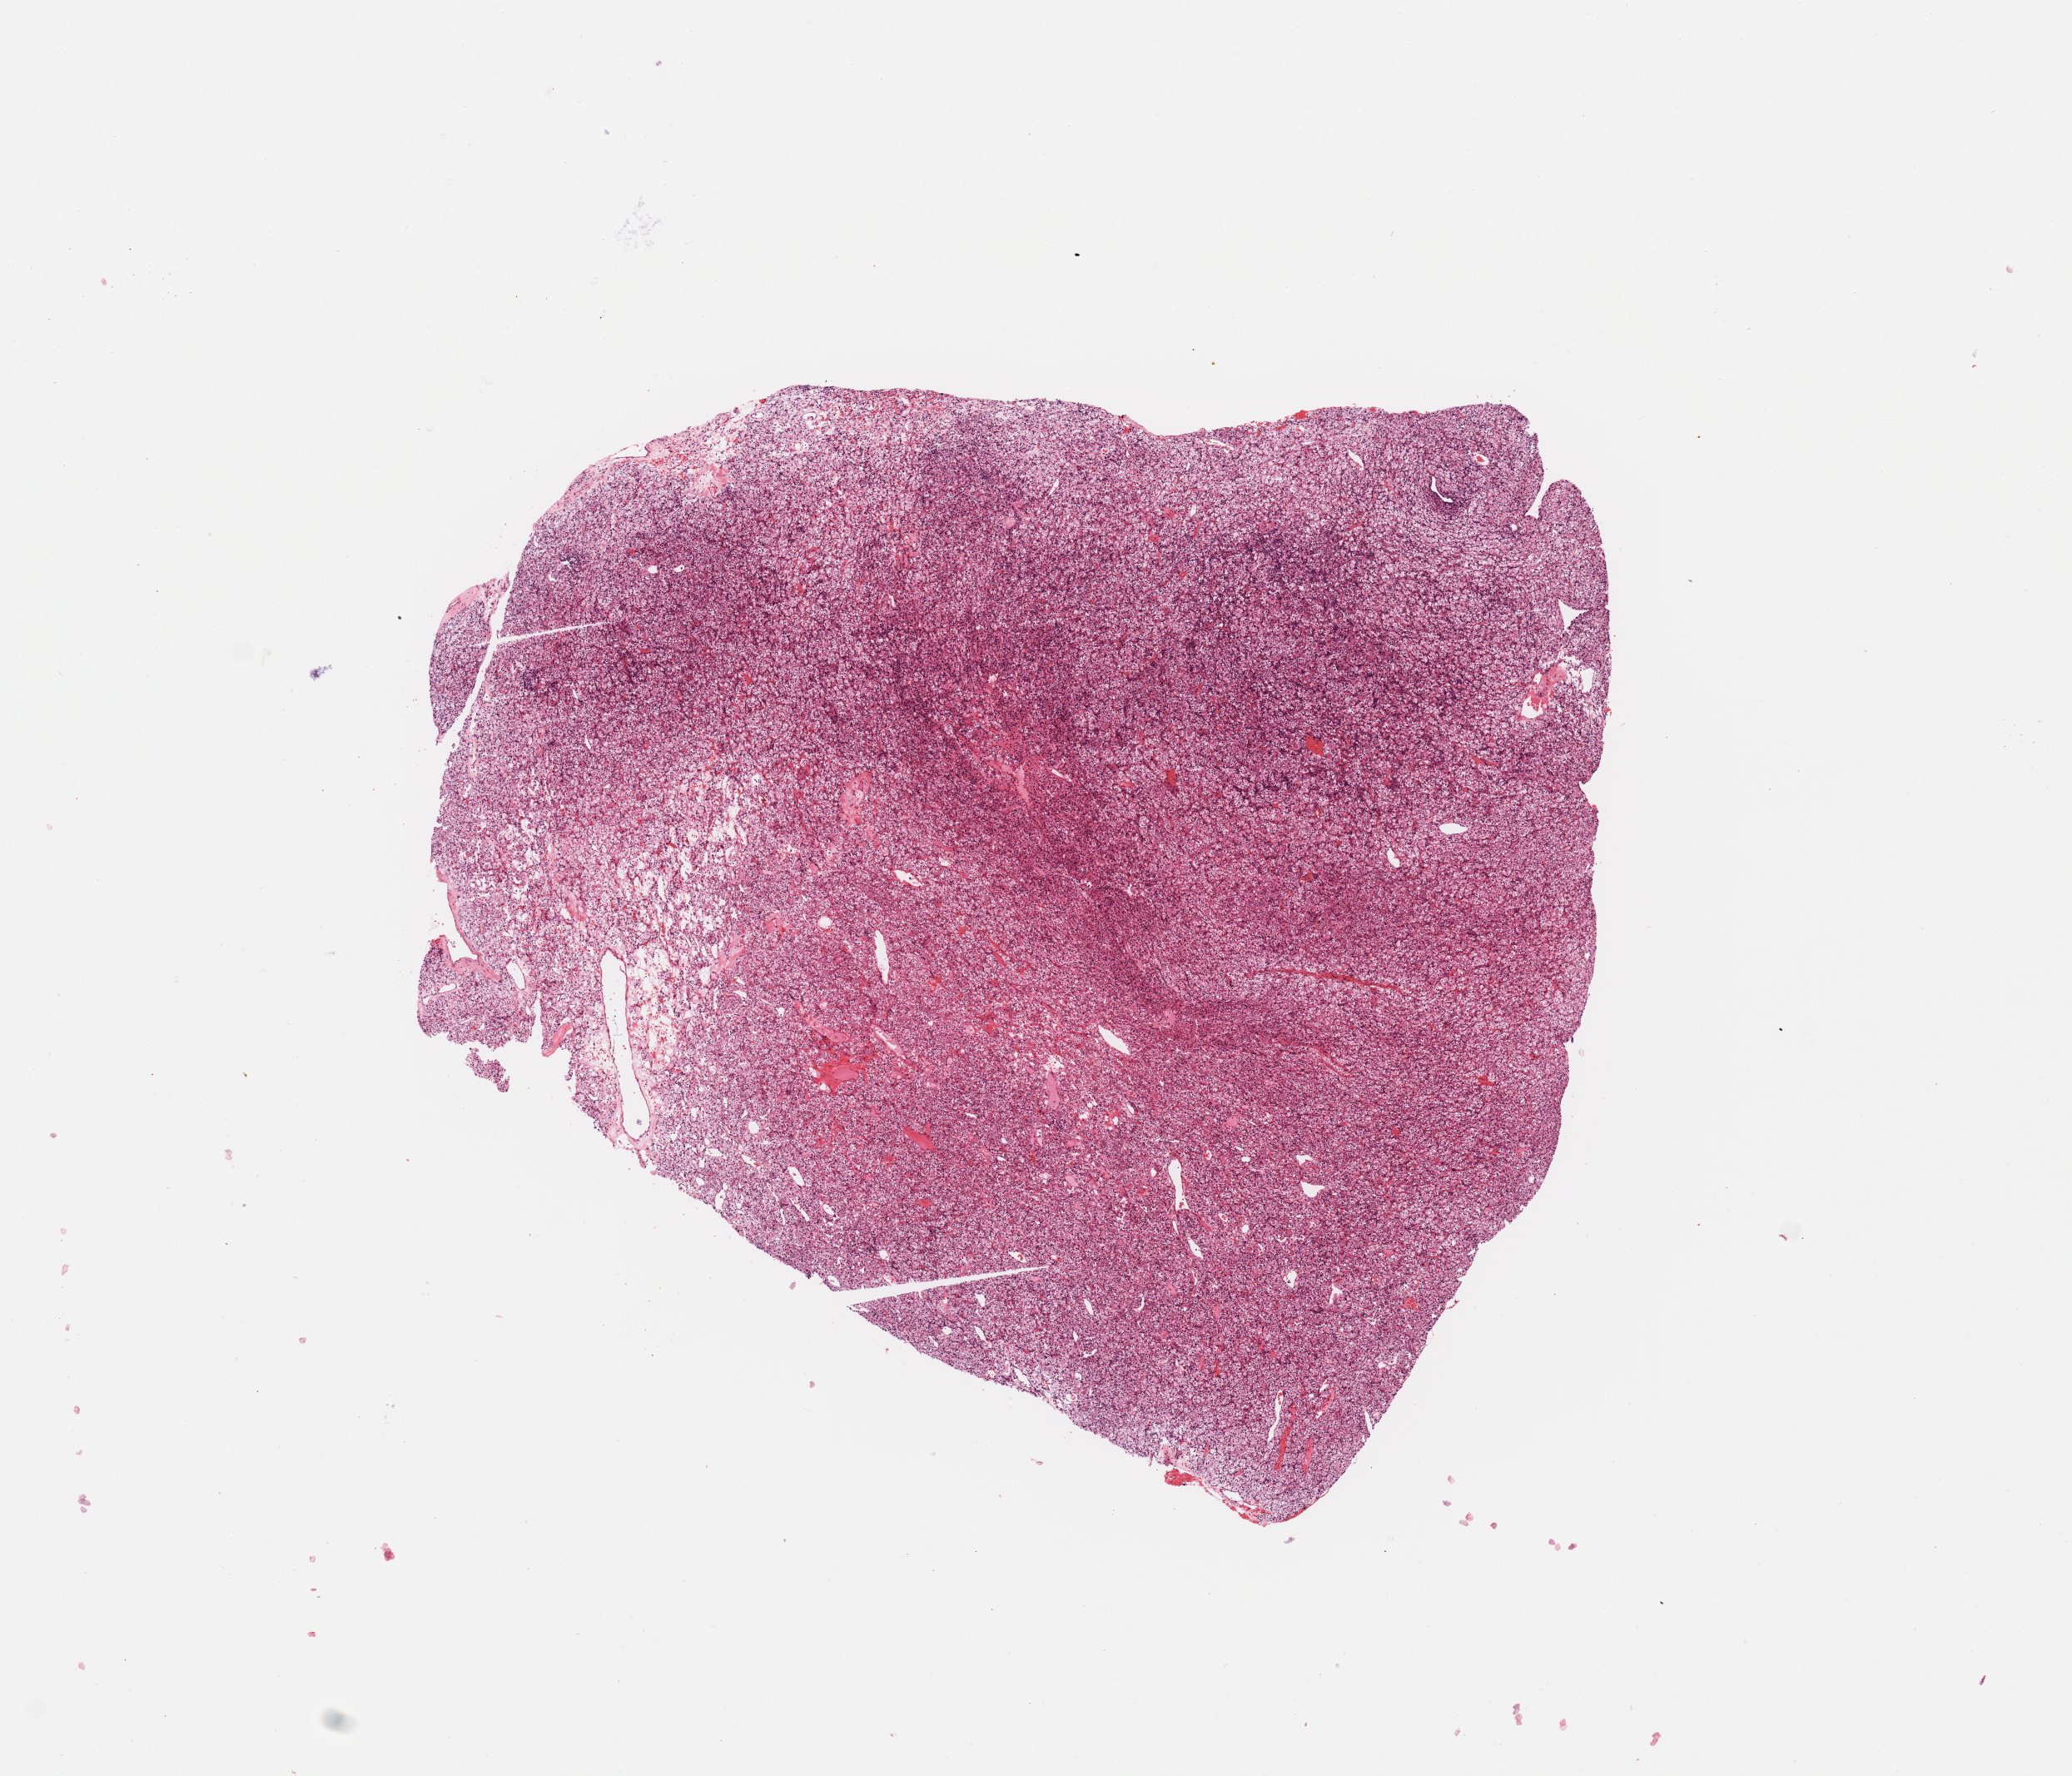
Whole-slide histology image, H&E-stained — a low-resolution overview of the entire scanned area, about 9.8 x 8.4 mm (slide scanned at 20x); tumour tissue sample, sampled site: kidney. Patient: female, age 61 years. Histologic grade: G2 (moderately differentiated). Slide review estimates, as recorded: tumour nuclei 90%, necrosis 2%.
- AJCC pathologic stage: II
- primary tumour site (as recorded): lower pole
- diagnosis: Renal cell carcinoma, NOS